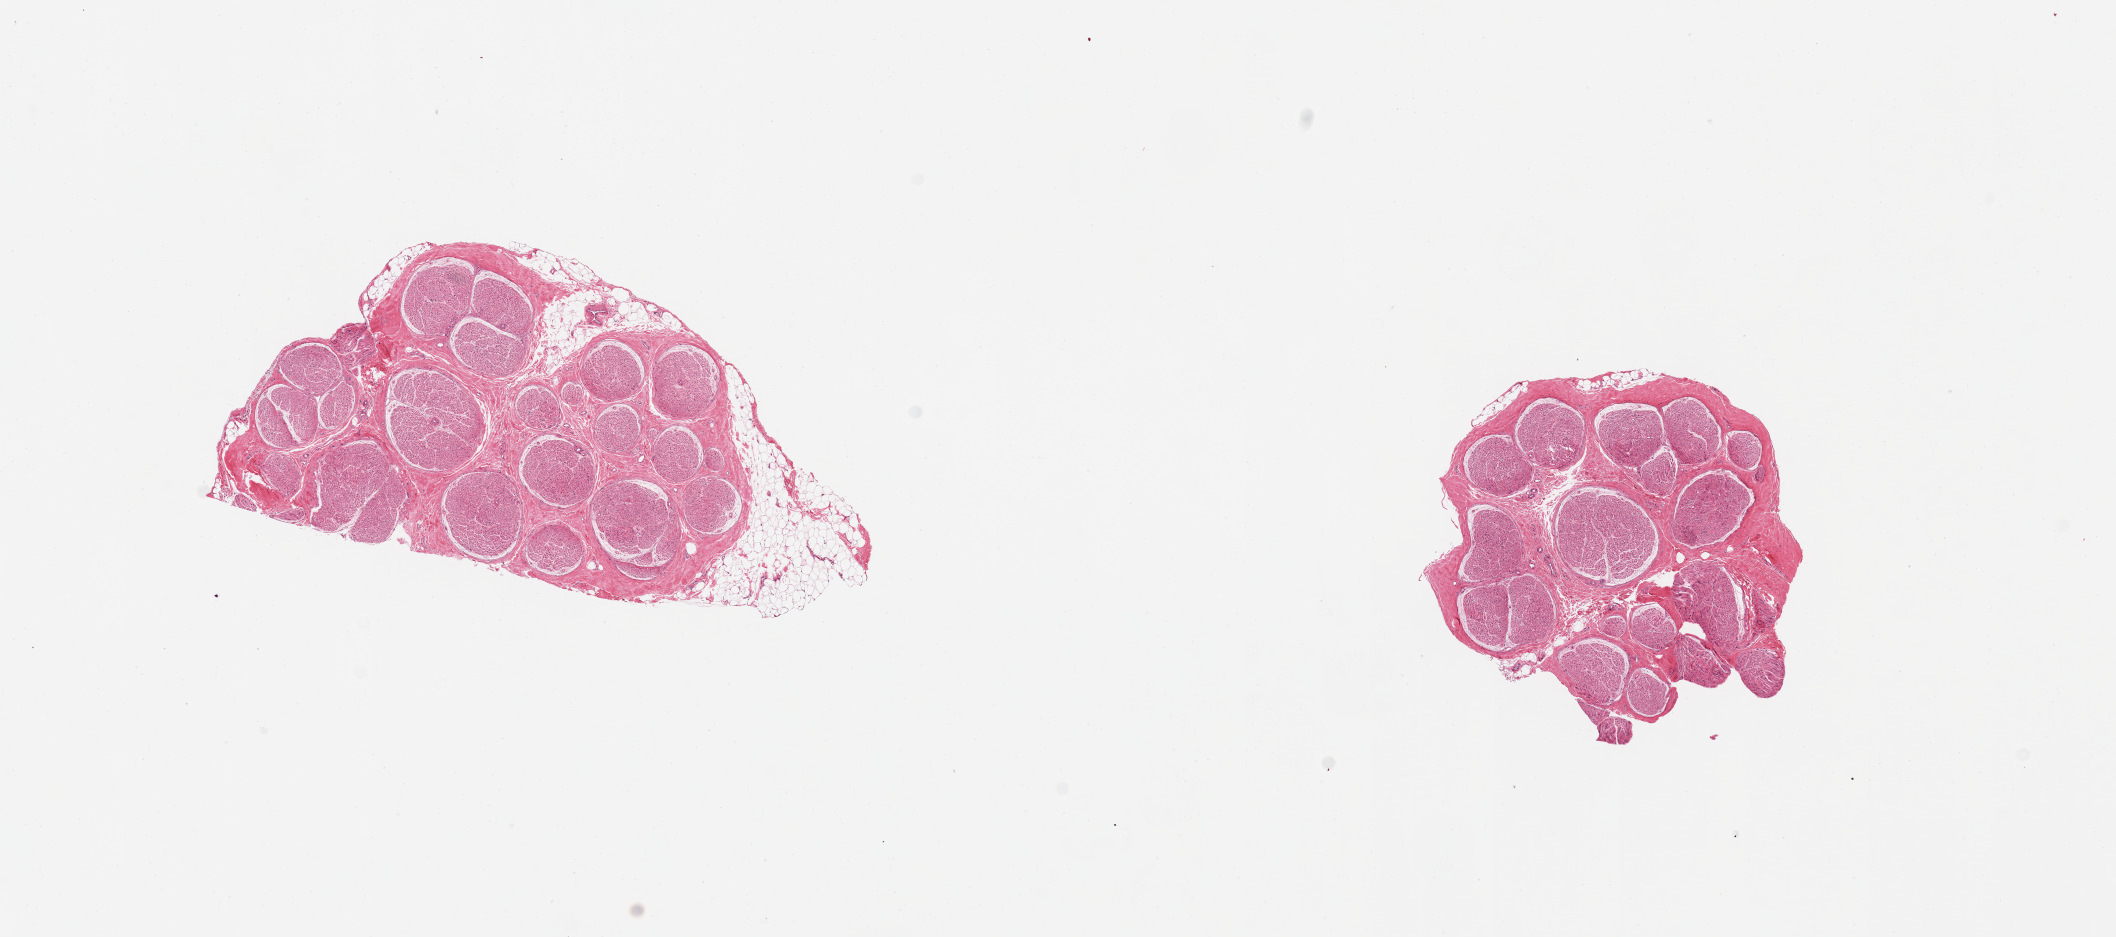
Haematoxylin and eosin whole-slide image, brightfield — shown as a low-resolution overview of the whole scanned area (about 16.7 x 7.4 mm). PAXgene-fixed, paraffin-embedded tissue. Sampled site (target tissue): tibial nerve. Tissue donor sample. Male donor.
Reviewer comment on this tissue sample: 2 pieces; well dissected except for 1x1 mm of external fat.